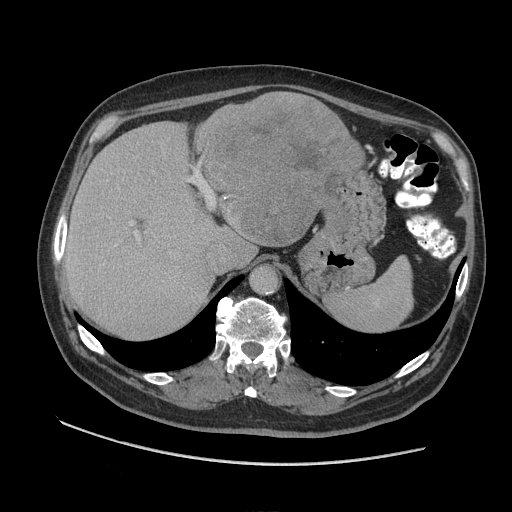
Contrast-enhanced abdominal CT (liver protocol), one axial slice. Slice 68 of 109 in the series (ordered by position). Reconstruction kernel STANDARD. Soft-tissue window (W 400 / L 40 HU). 512 × 512 image matrix, field of view 420 × 420 mm. From the clinical record (not read from this slice): diagnosis: hepatocellular carcinoma (patient treated with transarterial chemoembolisation; whether this scan precedes or follows treatment is not stated here); TNM stage (as recorded): Stage-I; Child-Pugh class: A.
Annotated regions visible in this slice (semi-automatically segmented with operator editing):
- liver parenchyma outside the tumour (the mass and vessels are separate outlines, so this box may not span the whole liver): bounding box <64,108,362,336> (left, top, right, bottom; pixels)
- mass: <194,91,363,247>
- liver vessels: <115,180,212,247>